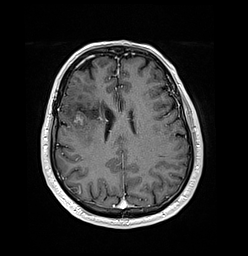
Brain MRI from a brain-tumour surgery series, one axial slice. Position 61 of 176 along the scan axis. T1-weighted post-contrast. 248 × 256 image matrix, field of view 242 × 250 mm. Case-level facts recorded for this patient, not image findings: histopathology: Oligodendroglioma; WHO grade: 3; IDH mutation: yes; tumour location: Right Frontal.
Structures marked on this image (expert manual segmentation):
- tumour: bounding box (x1, y1, x2, y2) in pixels: (73, 113, 84, 126)